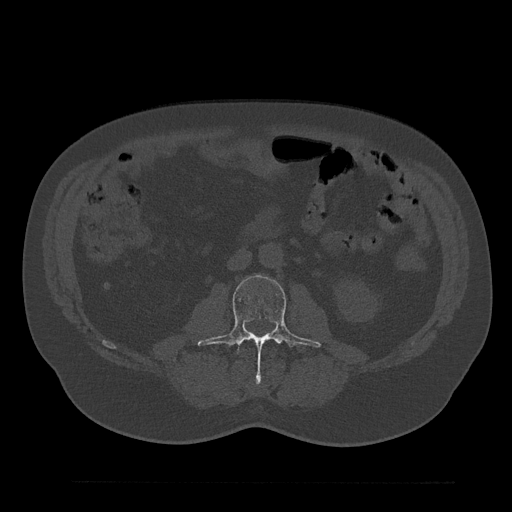
CT including the spine, one axial slice. Position 39 of 797 along the scan axis. Reconstruction kernel Br40s/3. 120 kVp. Bone window (W 1800 / L 400 HU). 0.5 mm slice thickness. 512 × 512 image matrix. Patient: male, 61 years. From the clinical record (not read from this slice): primary cancer: prostate.
Structures marked on this image (semi-automatic segmentation, software-assisted and operator-edited):
- L3 vertebra: bounding box (x1, y1, x2, y2) in pixels: (197, 275, 322, 380)